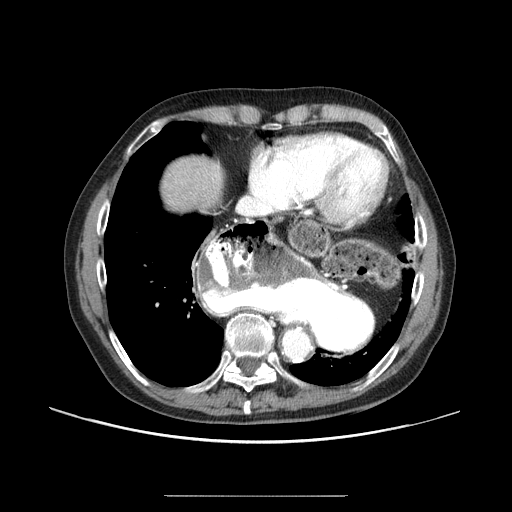
Contrast-enhanced abdominal CT (liver protocol), one axial slice; slice 80 of 91 in the series (ordered by position); one of 2 acquisitions stored at this slice position; soft-tissue window (W 400 / L 40 HU); 512 × 512 image matrix. Case-level facts recorded for this patient, not image findings: diagnosis: hepatocellular carcinoma (patient treated with transarterial chemoembolisation; whether this scan precedes or follows treatment is not stated here); TNM stage (as recorded): Stage-I; Child-Pugh class: A; tumour nodularity: uninodular.
Annotated regions visible in this slice (semi-automatic segmentation, software-assisted and operator-edited):
- liver parenchyma outside the tumour (the mass and vessels are separate outlines, so this box may not span the whole liver): bounding box <161,157,222,210> (left, top, right, bottom; pixels)